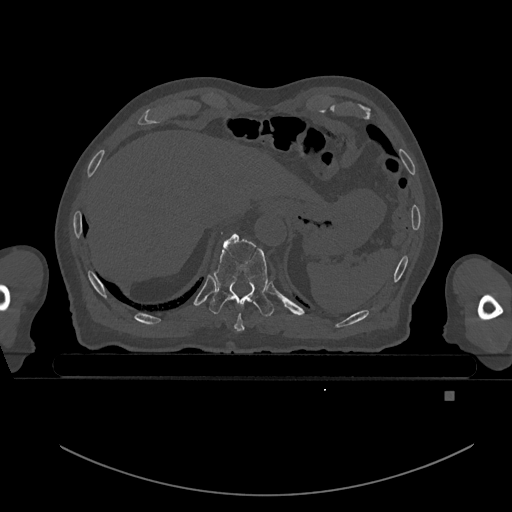
CT including the spine, one axial slice; slice 99 of 969 in the series (ordered by position); bone window (W 1800 / L 400 HU); 0.5 mm slice thickness; 512 × 512 image matrix. Patient: male, 82 years. From the clinical record (not read from this slice): primary cancer: prostate.
Annotated regions visible in this slice (semi-automatically segmented with operator editing):
- T10 vertebra: bounding box (x1, y1, x2, y2) in pixels: (209, 233, 274, 317)
- T9 vertebra: (234, 313, 245, 332)